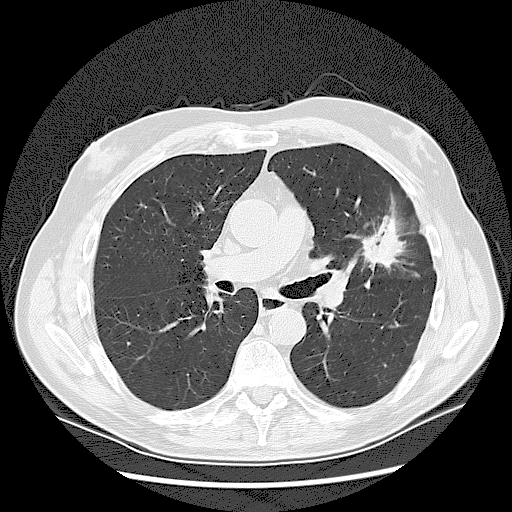
Axial slice from a low-dose chest CT screening exam. First (baseline) screen. Lung window (W 1500 / L -600 HU). 2.5 mm slice thickness. Lung (sharp) reconstruction kernel (LUNG). 120 kVp. Male participant, aged 65 years at enrolment. Current smoker at enrolment.
• Expert-annotated lung lesion, box from (x=350, y=225) to (x=398, y=270) px.
• Screening reader's record for this exam (one nodule recorded; not confirmed to be the boxed lesion): non-calcified nodule or mass ≥4 mm, left upper lobe, 37 × 27 mm, spiculated (stellate) margins, soft tissue attenuation.
• Official screen result: positive, change unspecified: nodule(s) >= 4 mm or enlarging nodule(s), mass(es), or other non-specific abnormalities suspicious for lung cancer.
• Later outcome: lung cancer diagnosed 56 days after this screen — non-small cell carcinoma, poorly differentiated (G3), stage IA (AJCC 6th edition).